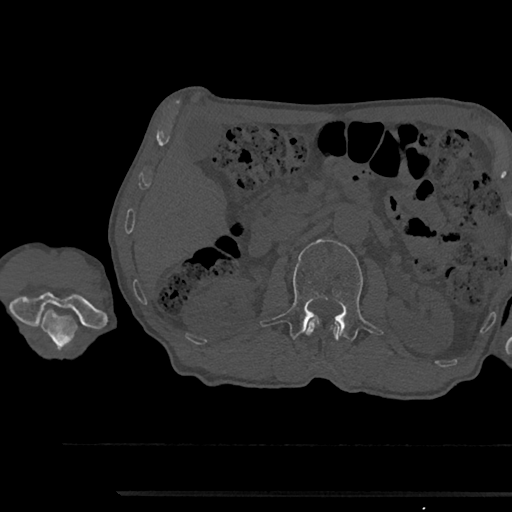
CT including the spine, one axial slice; position 583 of 797 along the scan axis; reconstruction kernel Br40s/3; bone window (W 1800 / L 400 HU); 0.5 mm slice thickness; 512 × 512 image matrix, field of view 367 × 367 mm. Patient: male, 79 years. From the clinical record (not read from this slice): primary cancer: prostate.
Structures marked on this image (semi-automatic segmentation, software-assisted and operator-edited):
- L1 vertebra: bounding box [x1, y1, x2, y2] px = [305, 318, 343, 341]
- L2 vertebra: [260, 239, 381, 340]